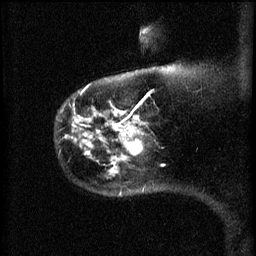
Breast MRI (dynamic contrast-enhanced), one sagittal slice. Slice 52 of 60 in the series (ordered by position). 3 images stored at this slice position (order not interpretable as contrast timing). 1.5 T. TE 4.2 ms, TR 11 ms. 256 × 256 image matrix. Patient: female, 44 years.
Structures marked on this image (semi-automatically segmented with operator editing):
- analysis volume of interest (the breast-tissue region the enhancement analysis was run in; not a lesion): bounding box (x1, y1, x2, y2) in pixels: (114, 124, 149, 173)
- tumour enhancement mask (voxels above the 70 % enhancement threshold inside the analysis volume of interest): (114, 124, 143, 173)